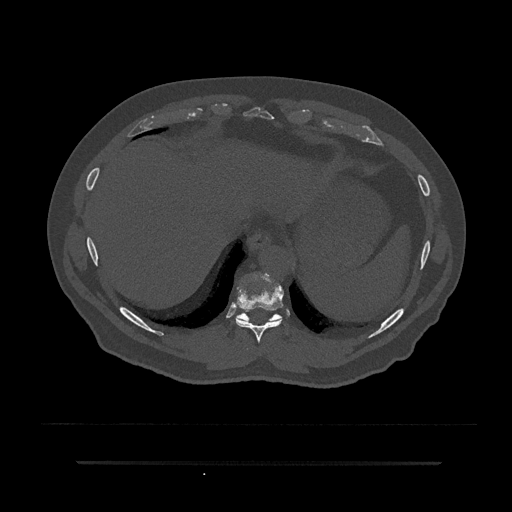
CT including the spine, one axial slice; position 360 of 797 along the scan axis; bone window (W 1800 / L 400 HU); 0.5 mm slice thickness; 512 × 512 image matrix, field of view 464 × 464 mm. Patient: male, 59 years. Case-level facts recorded for this patient, not image findings: primary cancer: bile ducts.
Outlined on this slice (semi-automatic segmentation, software-assisted and operator-edited):
- T10 vertebra: box from (x=236, y=285) to (x=281, y=325) px
- T9 vertebra: (x=236, y=273)–(x=284, y=342)